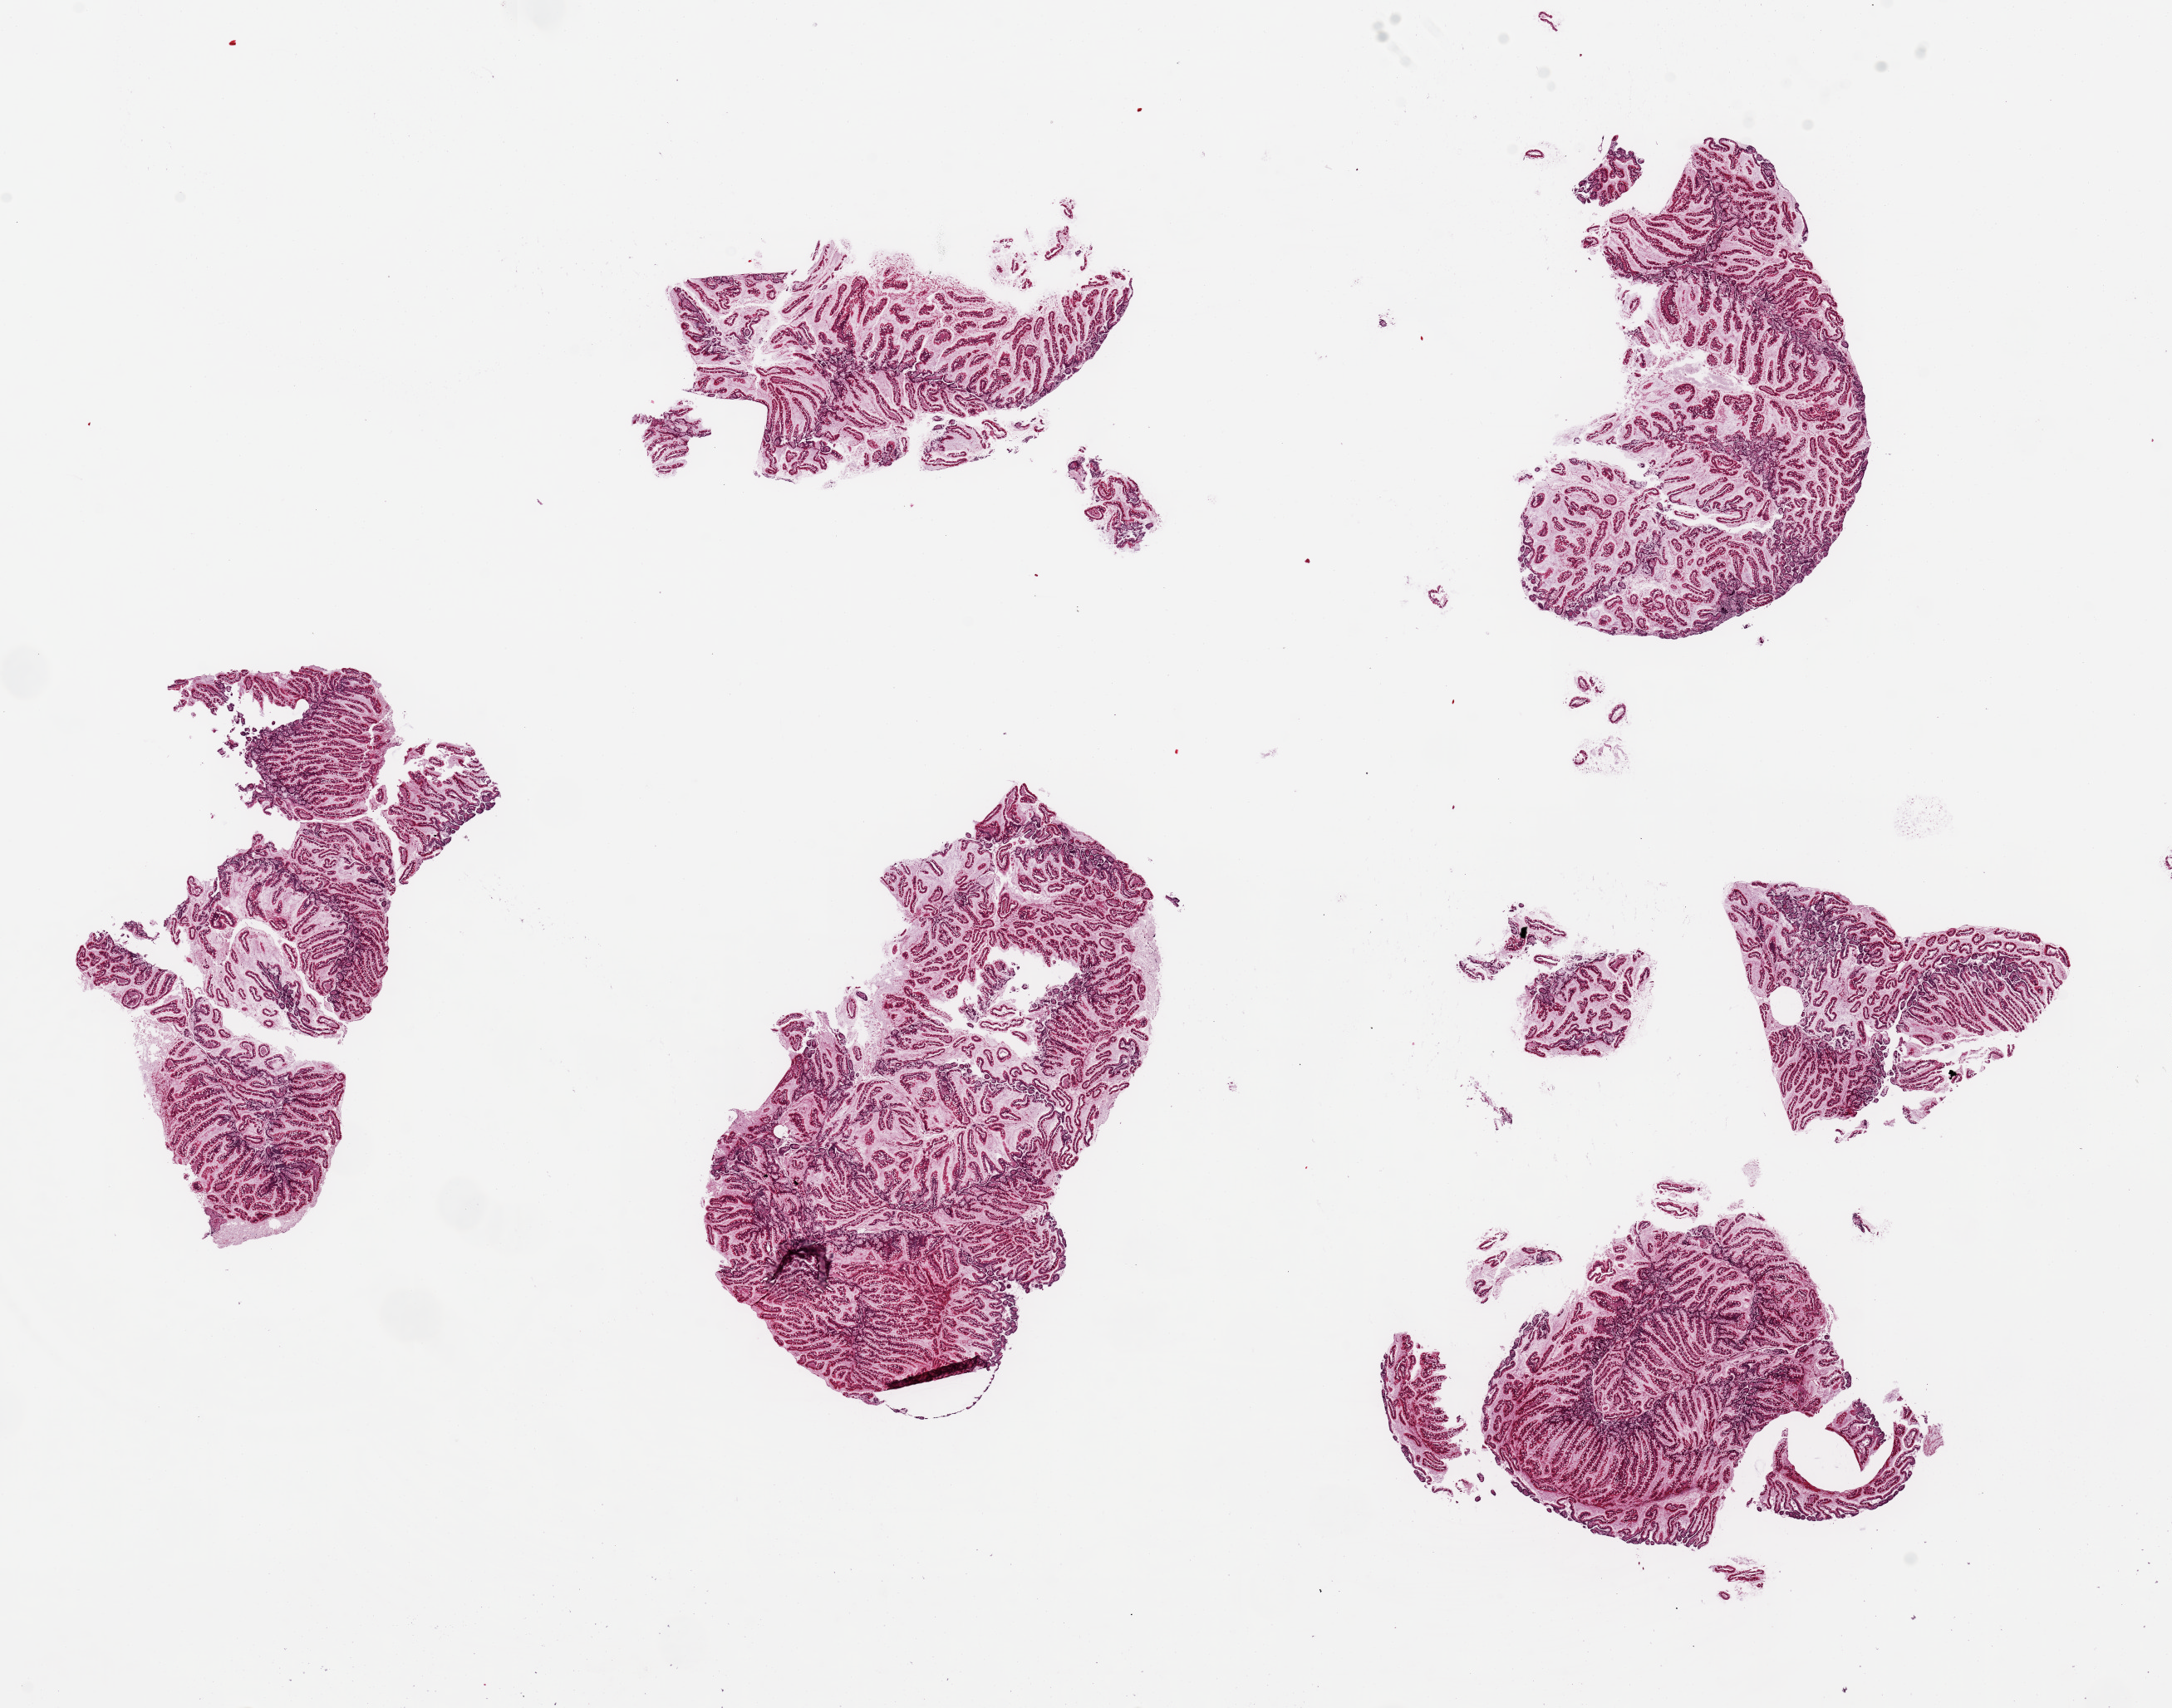
H&E whole-slide image, brightfield, shown as a low-resolution overview of the whole scanned area (about 20.7 x 16.3 mm), PAXgene-fixed paraffin-embedded (PFPE) section, sampled site (target tissue): ileum, tissue donor sample. Donor: female.
Review note (as recorded): 6 pieces, up to 7x6mm. Well preserved ileal mucosa without lymphoid tissue.